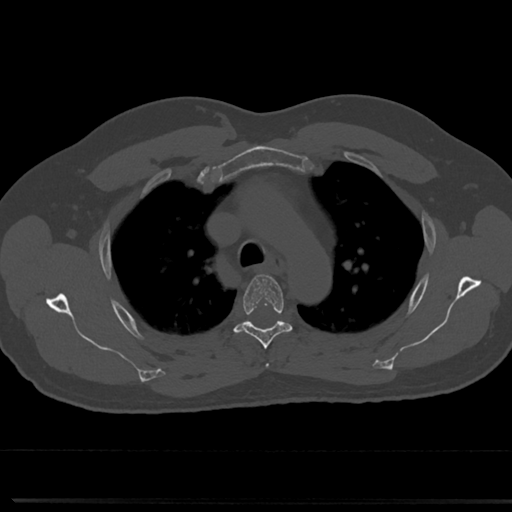
CT including the spine, one axial slice. Position 546 of 817 along the scan axis. Reconstruction kernel Br40s/3. 120 kVp. Bone window (W 1800 / L 400 HU). 0.5 mm slice thickness. 512 × 512 image matrix, field of view 355 × 355 mm. Male patient, age 61 years. From the clinical record (not read from this slice): primary cancer: prostate.
Annotated regions visible in this slice (semi-automatic segmentation, software-assisted and operator-edited):
- T3 vertebra: bounding box [x1, y1, x2, y2] px = [266, 364, 269, 368]
- T4 vertebra: [233, 274, 293, 349]